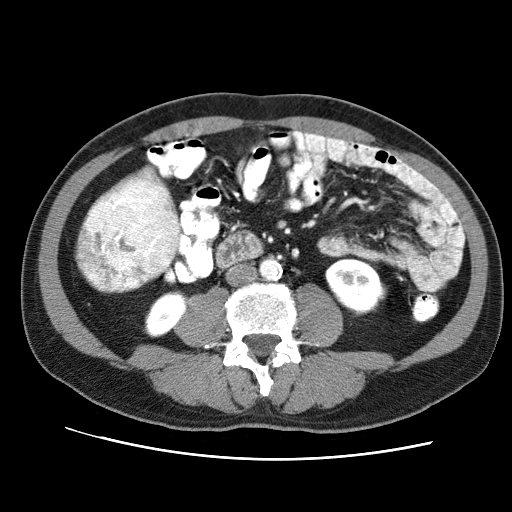
Contrast-enhanced abdominal CT (liver protocol), one axial slice; slice 11 of 71 in the series (ordered by position); reconstruction kernel STANDARD; soft-tissue window (W 400 / L 40 HU); 2.5 mm slice thickness; 512 × 512 image matrix. From the clinical record (not read from this slice): diagnosis: hepatocellular carcinoma (patient treated with transarterial chemoembolisation; whether this scan precedes or follows treatment is not stated here); TNM stage (as recorded): Stage-II; Child-Pugh class: A; tumour nodularity: multinodular.
Annotated regions visible in this slice (semi-automatic segmentation, software-assisted and operator-edited):
- liver parenchyma outside the tumour (the mass and vessels are separate outlines, so this box may not span the whole liver): bounding box <75,165,183,293> (left, top, right, bottom; pixels)
- mass: <75,200,164,292>
- liver vessels: <109,175,181,267>